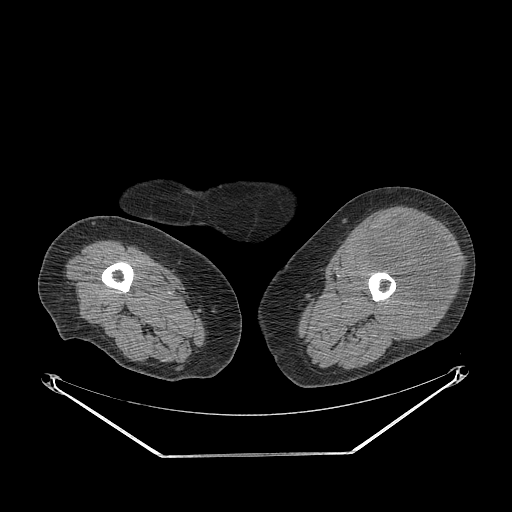
CT of an extremity soft-tissue mass (from a PET/CT study), one axial slice. Position 222 of 267 along the scan axis. Reconstruction kernel STANDARD. 140 kVp. Soft-tissue window (W 400 / L 40 HU). 3.75 mm slice thickness. 512 × 512 image matrix, field of view 500 × 500 mm. Female patient. Case-level facts recorded for this patient, not image findings: histological type: undifferentiated – high grade; grade: high; site of the primary tumour: left thigh.
Outlined on this slice (expert contour drawn on MRI and transferred to this co-registered scan by the dataset authors):
- gross tumour volume including surrounding oedema: box from (x=356, y=217) to (x=453, y=339) px
- gross tumour volume (mass): (x=356, y=217)–(x=453, y=339)